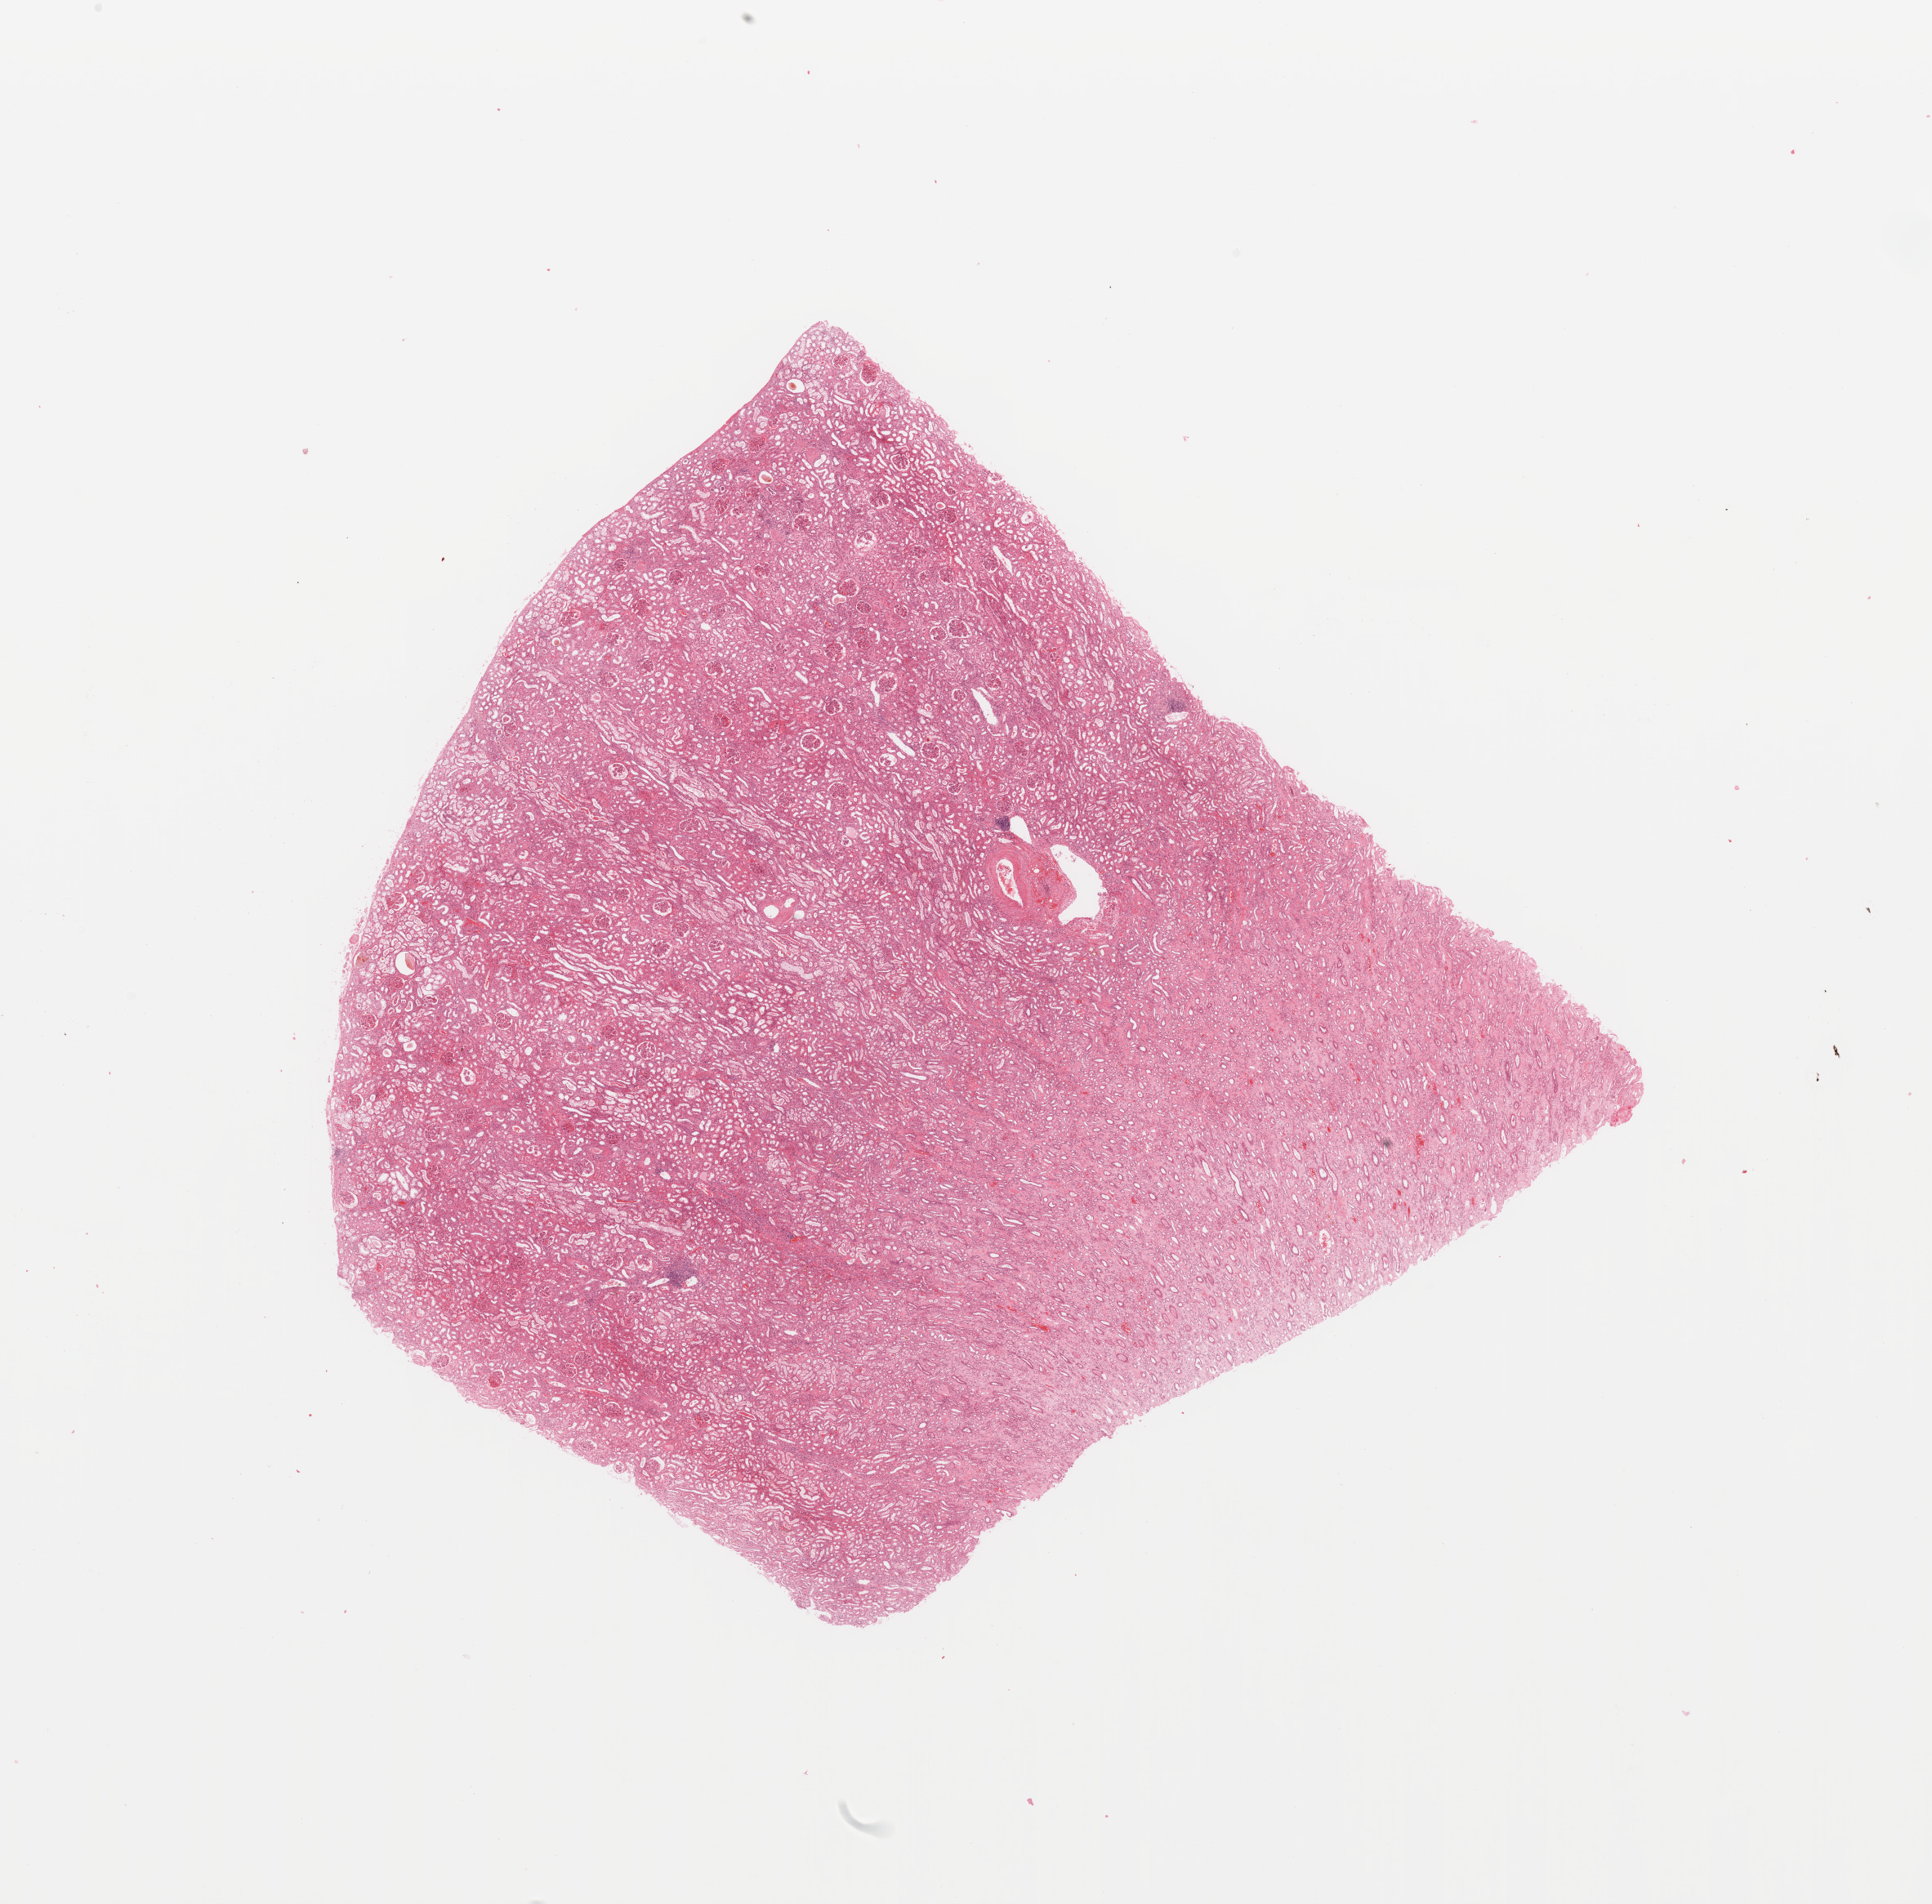
Hematoxylin and eosin (H&E) stained whole-slide image, a low-resolution overview of the entire scanned area, about 18.7 x 18.4 mm. Kidney, normal (non-tumour) tissue. Patient: female, age 68 years.
This section: normal (non-tumour) tissue from the same patient. Patient diagnosis: Renal cell carcinoma, NOS.